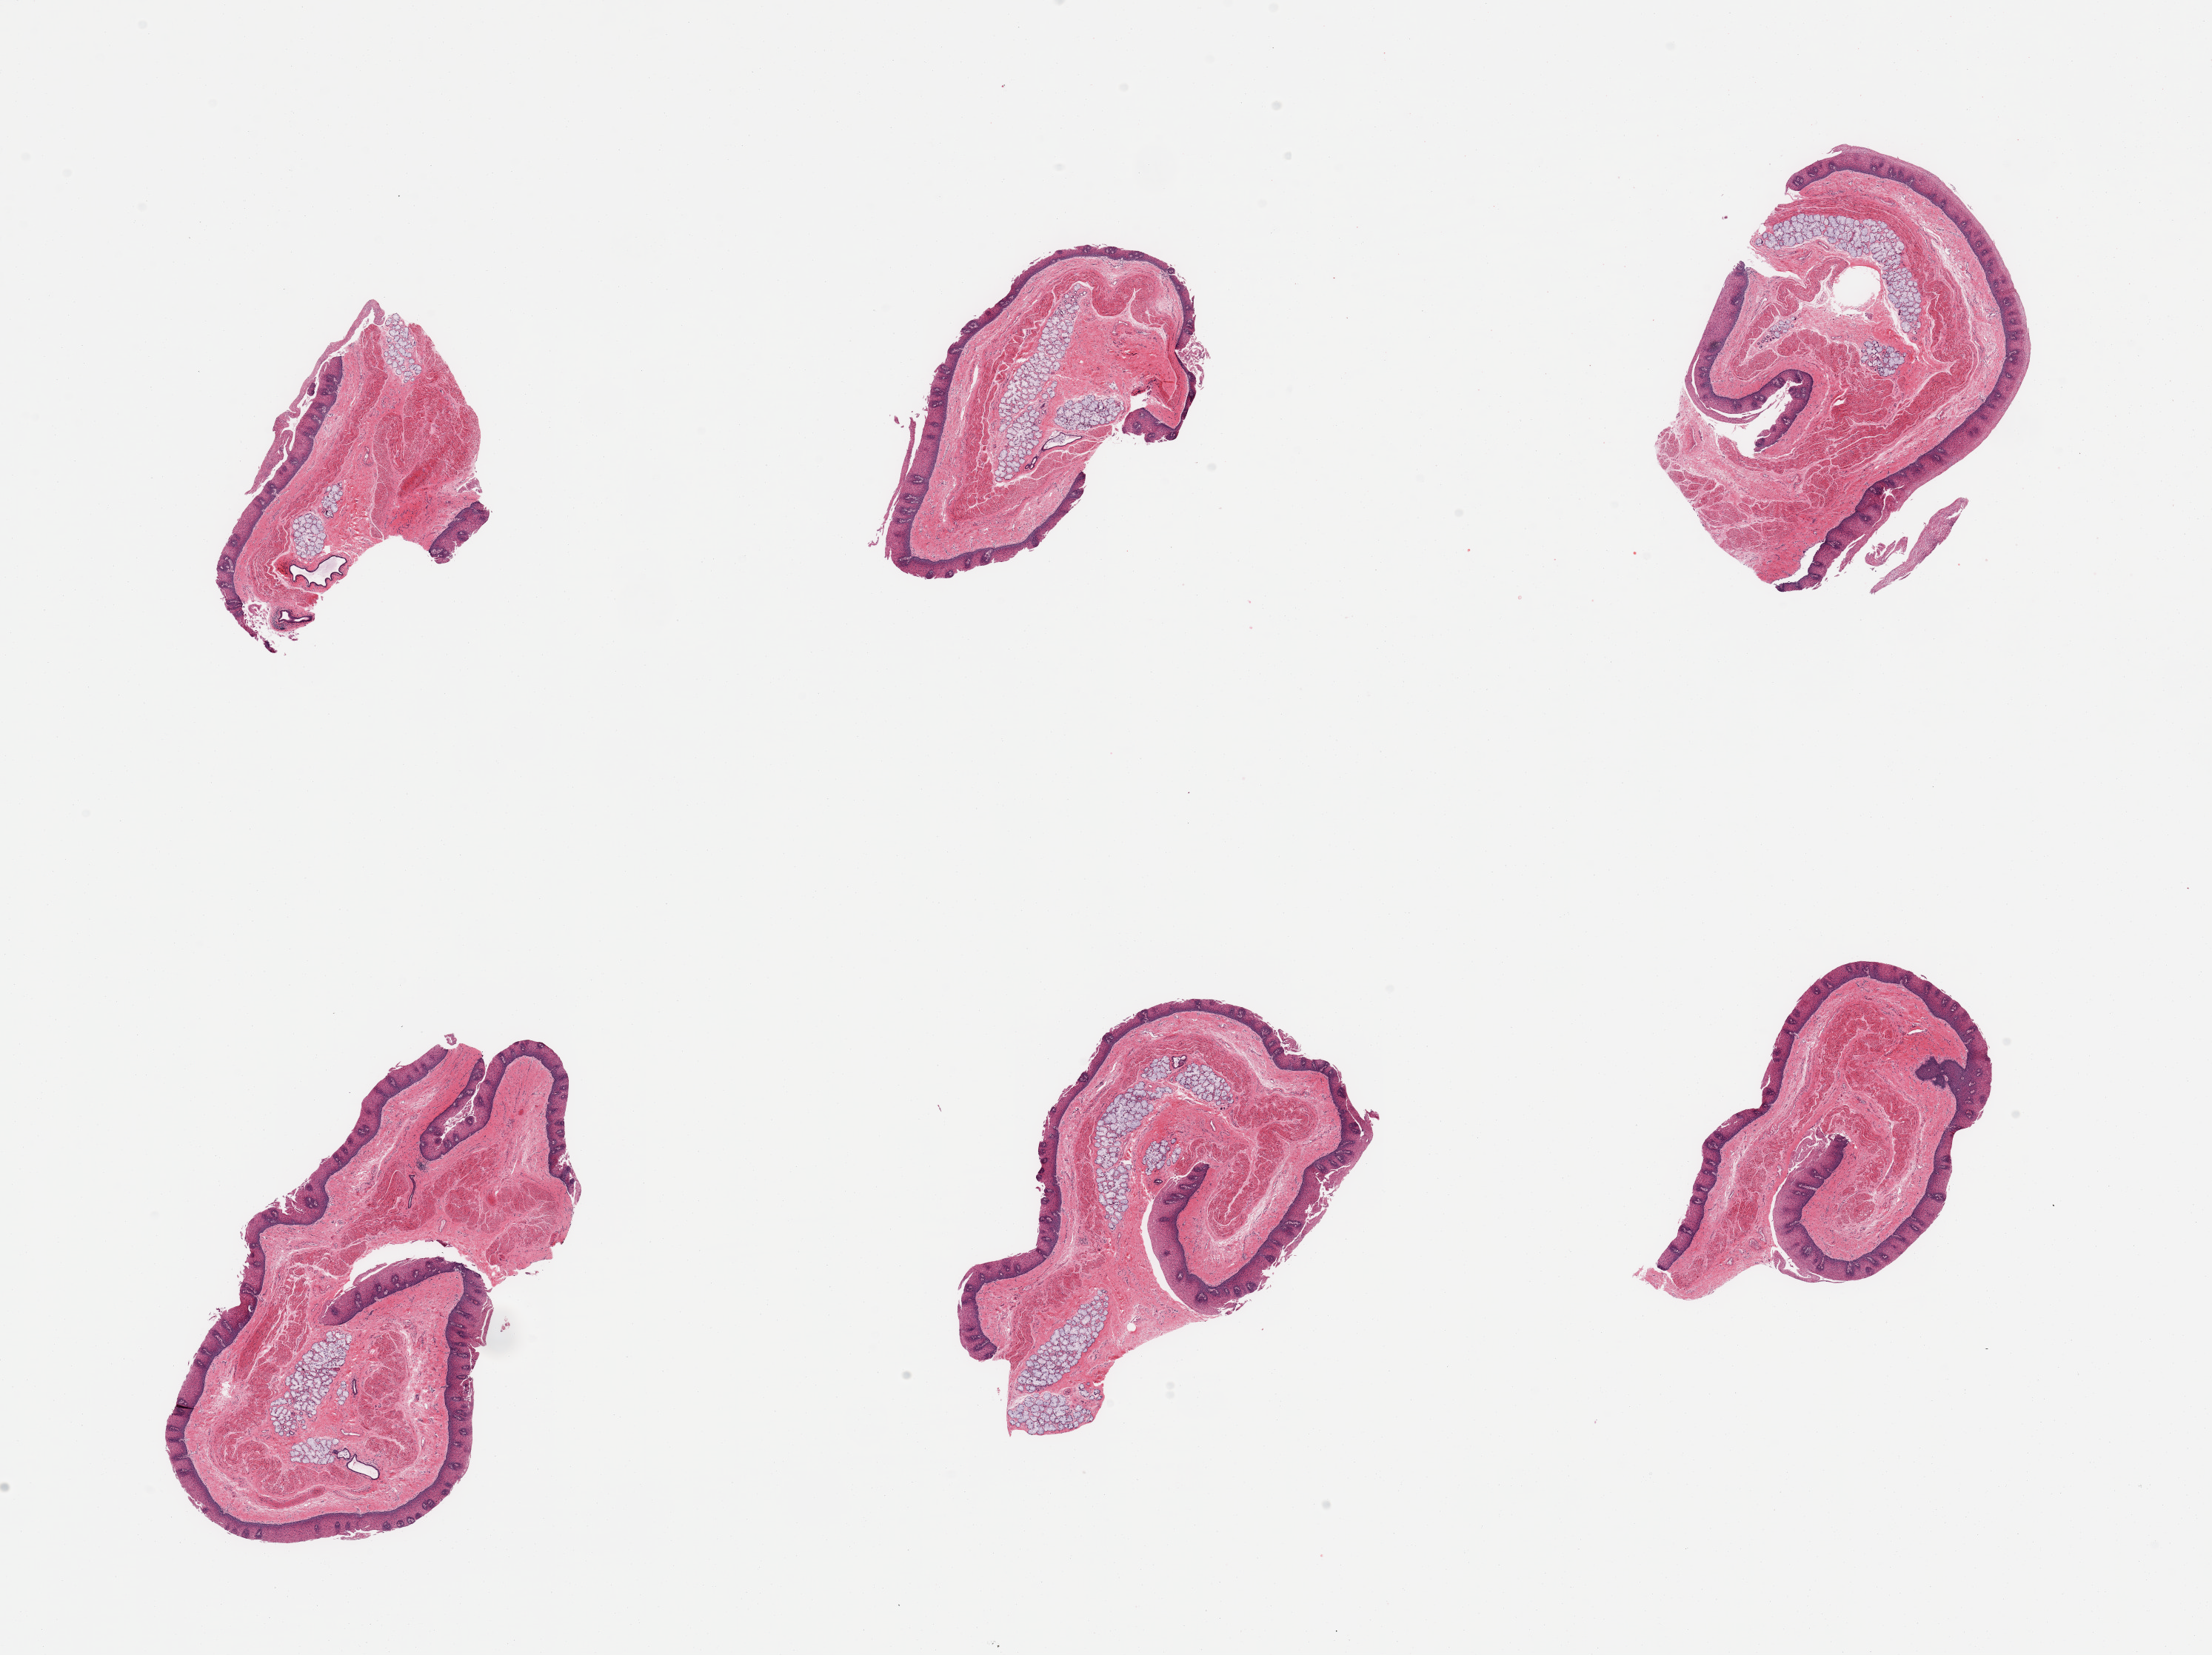
Hematoxylin and eosin (H&E) whole-slide image — low-resolution overview of the scanned area, about 23.6 x 17.7 mm (acquisition: 20x scan); PAXgene-fixed paraffin-embedded (PFPE) section; section of esophageal mucous membrane (target tissue); donor tissue sample.
Review note (as recorded): 6 pieces; prominent submucosal mucous glands in 5 pieces occupying up to 25%.